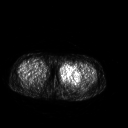
FDG PET of an extremity soft-tissue mass (from a PET/CT study), one axial slice; slice 237 of 267 in the series (ordered by position); 3.27 mm slice thickness; 128 × 128 image matrix, field of view 500 × 500 mm. Patient: female, 42 years. Case-level facts recorded for this patient, not image findings: histological type: pleiomorphic leiomyosarcoma; grade: intermediate; site of the primary tumour: left thigh.
Outlined on this slice (expert contour drawn on MRI and transferred to this co-registered scan by the dataset authors):
- gross tumour volume including surrounding oedema: bounding box <59,64,83,83> (left, top, right, bottom; pixels)
- gross tumour volume (mass): <59,64,82,83>